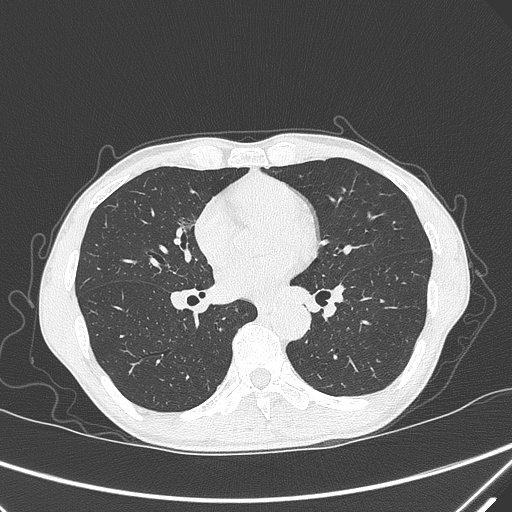
Chest CT, one axial slice. Position 160 of 339 along the scan axis. Lung window (W 1500 / L -600 HU). 1 mm slice thickness. 512 × 512 image matrix, field of view 350 × 350 mm. Male patient, age 67 years. From the clinical record (not read from this slice): clinical TNM (as recorded): T1c N0 M0; histopathological grade: G1-2.
Structures marked on this image (rectangle marked by the reading radiologist):
- lung tumour (recorded histology: adenocarcinoma): bounding box (x1, y1, x2, y2) in pixels: (170, 209, 199, 244)